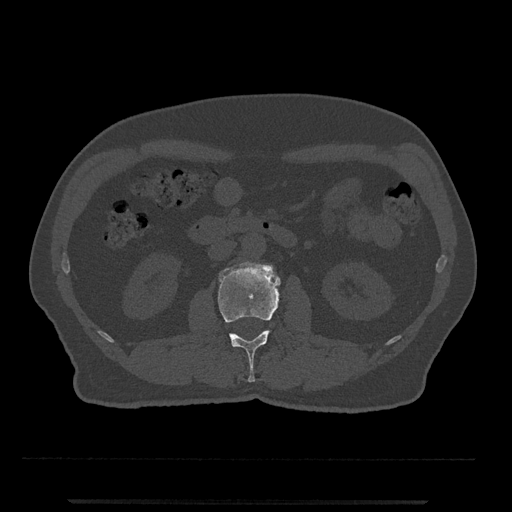
CT including the spine, one axial slice; slice 258 of 797 in the series (ordered by position); bone window (W 1800 / L 400 HU); 512 × 512 image matrix. Patient: male, 63 years. Case-level facts recorded for this patient, not image findings: primary cancer: prostate.
Structures marked on this image (semi-automatically segmented with operator editing):
- L2 vertebra: bounding box <218,261,281,382> (left, top, right, bottom; pixels)